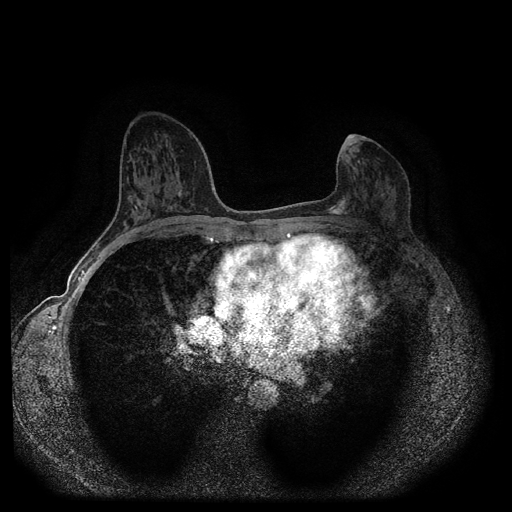
Breast MRI (dynamic contrast-enhanced, multi-phase), one axial slice; slice 51 of 116 in the series (ordered by position); dynamic contrast-enhanced series, time point 2 of 5 at this slice position (early post-contrast); 1.5 T; TE 2.6 ms, TR 5.4 ms; 2 mm slice thickness; 512 × 512 image matrix. Female patient, age 57 years.
Outlined on this slice (semi-automatically segmented with operator editing):
- breast lesion (labelled 'tumour' in the annotation; benign lesions carry a separate 'benign' label): box from (x=328, y=196) to (x=348, y=217) px